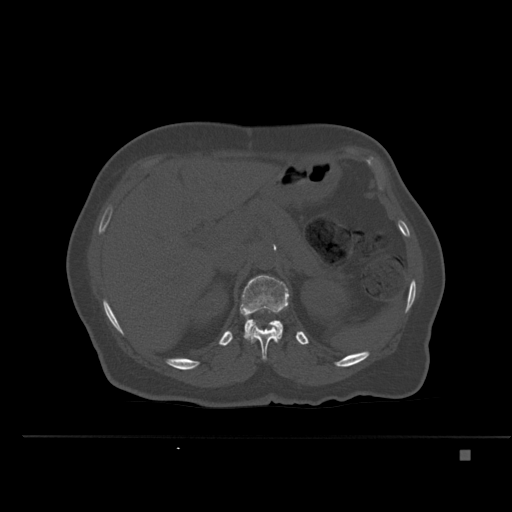
CT including the spine, one axial slice; position 246 of 477 along the scan axis; bone window (W 1800 / L 400 HU); 1.5 mm slice thickness; 512 × 512 image matrix, field of view 422 × 422 mm. Patient: female, 74 years. From the clinical record (not read from this slice): primary cancer: colon.
Structures marked on this image (semi-automatically segmented with operator editing):
- L1 vertebra: bounding box <240,275,290,341> (left, top, right, bottom; pixels)
- T12 vertebra: <249,324,279,360>